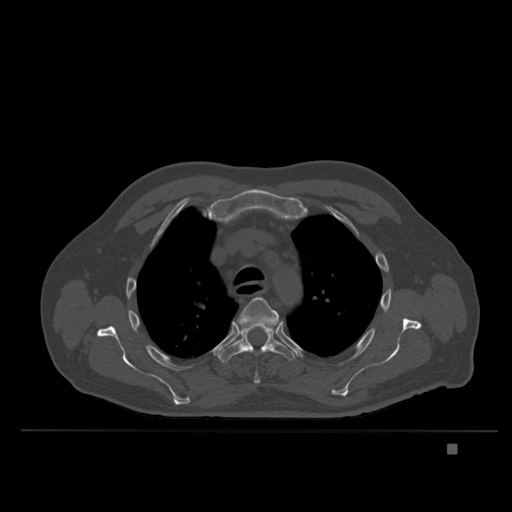
CT including the spine, one axial slice; slice 280 of 435 in the series (ordered by position); bone window (W 1800 / L 400 HU); 1.5 mm slice thickness; 512 × 512 image matrix, field of view 434 × 434 mm. Patient: male, 73 years. Case-level facts recorded for this patient, not image findings: primary cancer: skin.
Outlined on this slice (semi-automatically segmented with operator editing):
- T4 vertebra: bounding box (x1, y1, x2, y2) in pixels: (239, 297, 279, 384)
- T5 vertebra: (220, 322, 295, 363)